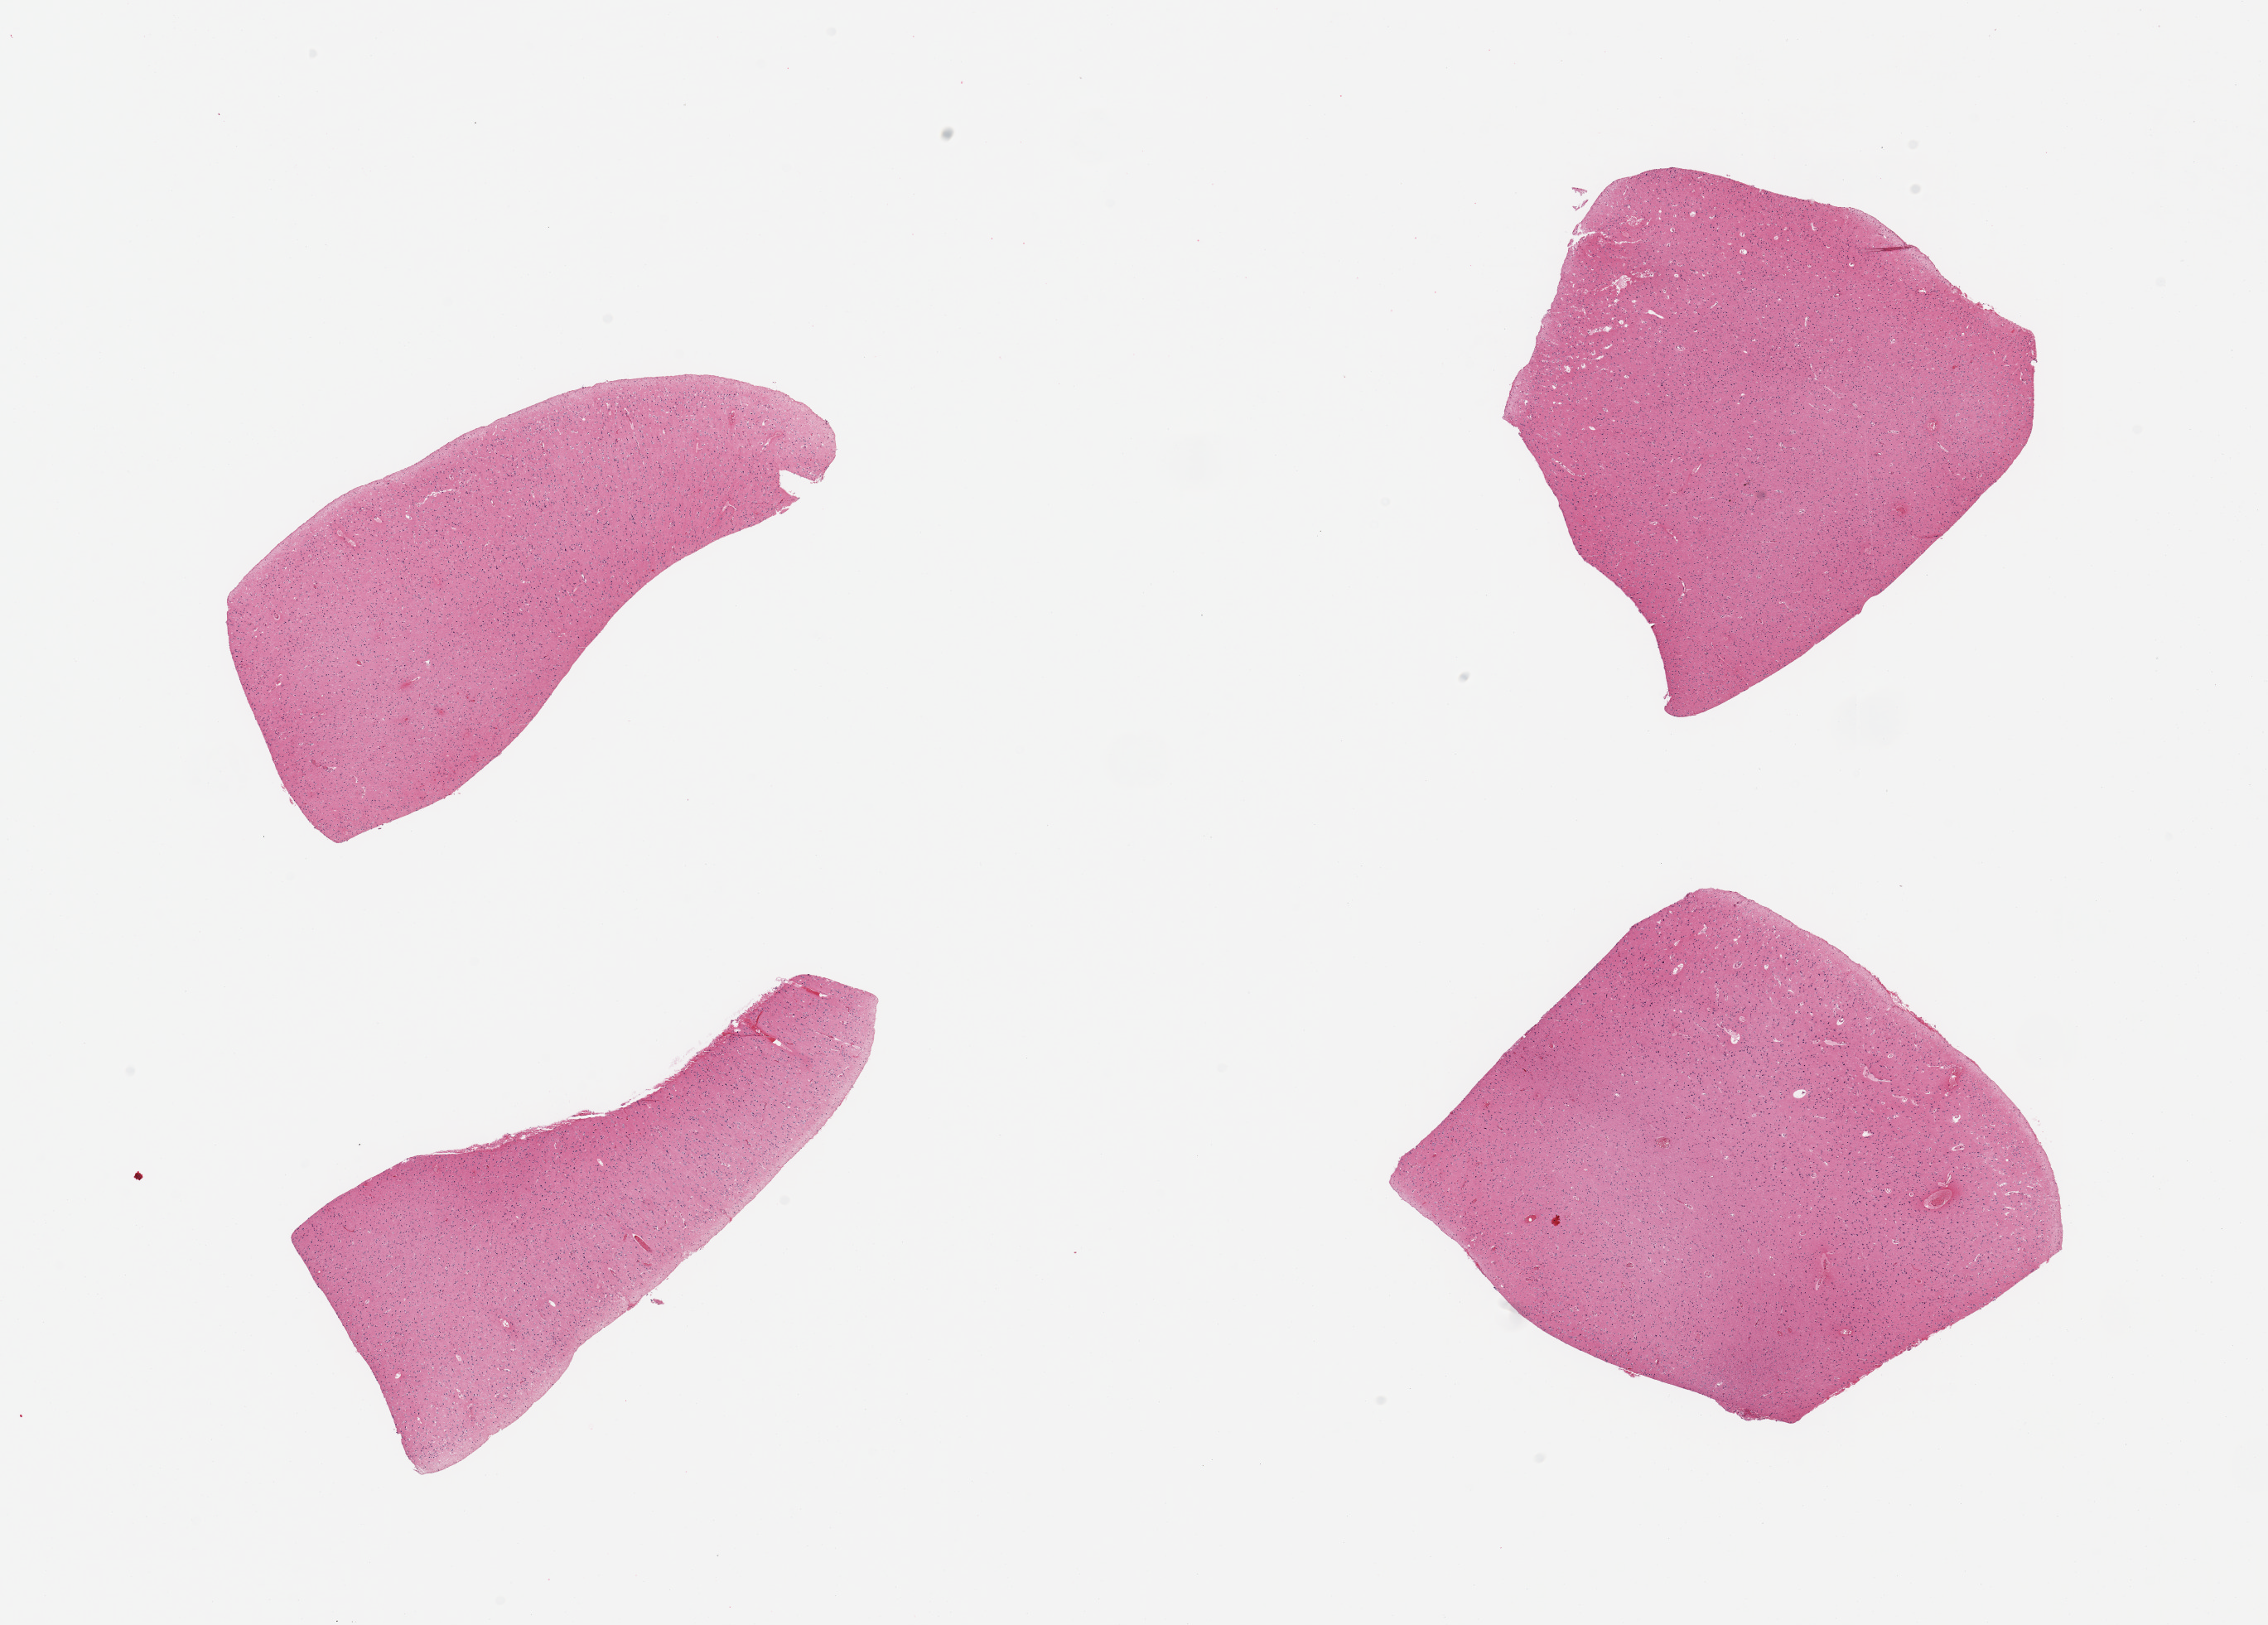
H&E whole-slide image, a low-resolution overview of the entire scanned area, about 21.7 x 15.5 mm (acquisition: 20x scan); PAXgene-fixed, paraffin-embedded tissue; target tissue: cerebral cortex; tissue donor sample. Male donor.
Reviewer comment on this tissue sample: 4 pieces; mild to moderate autolysis.